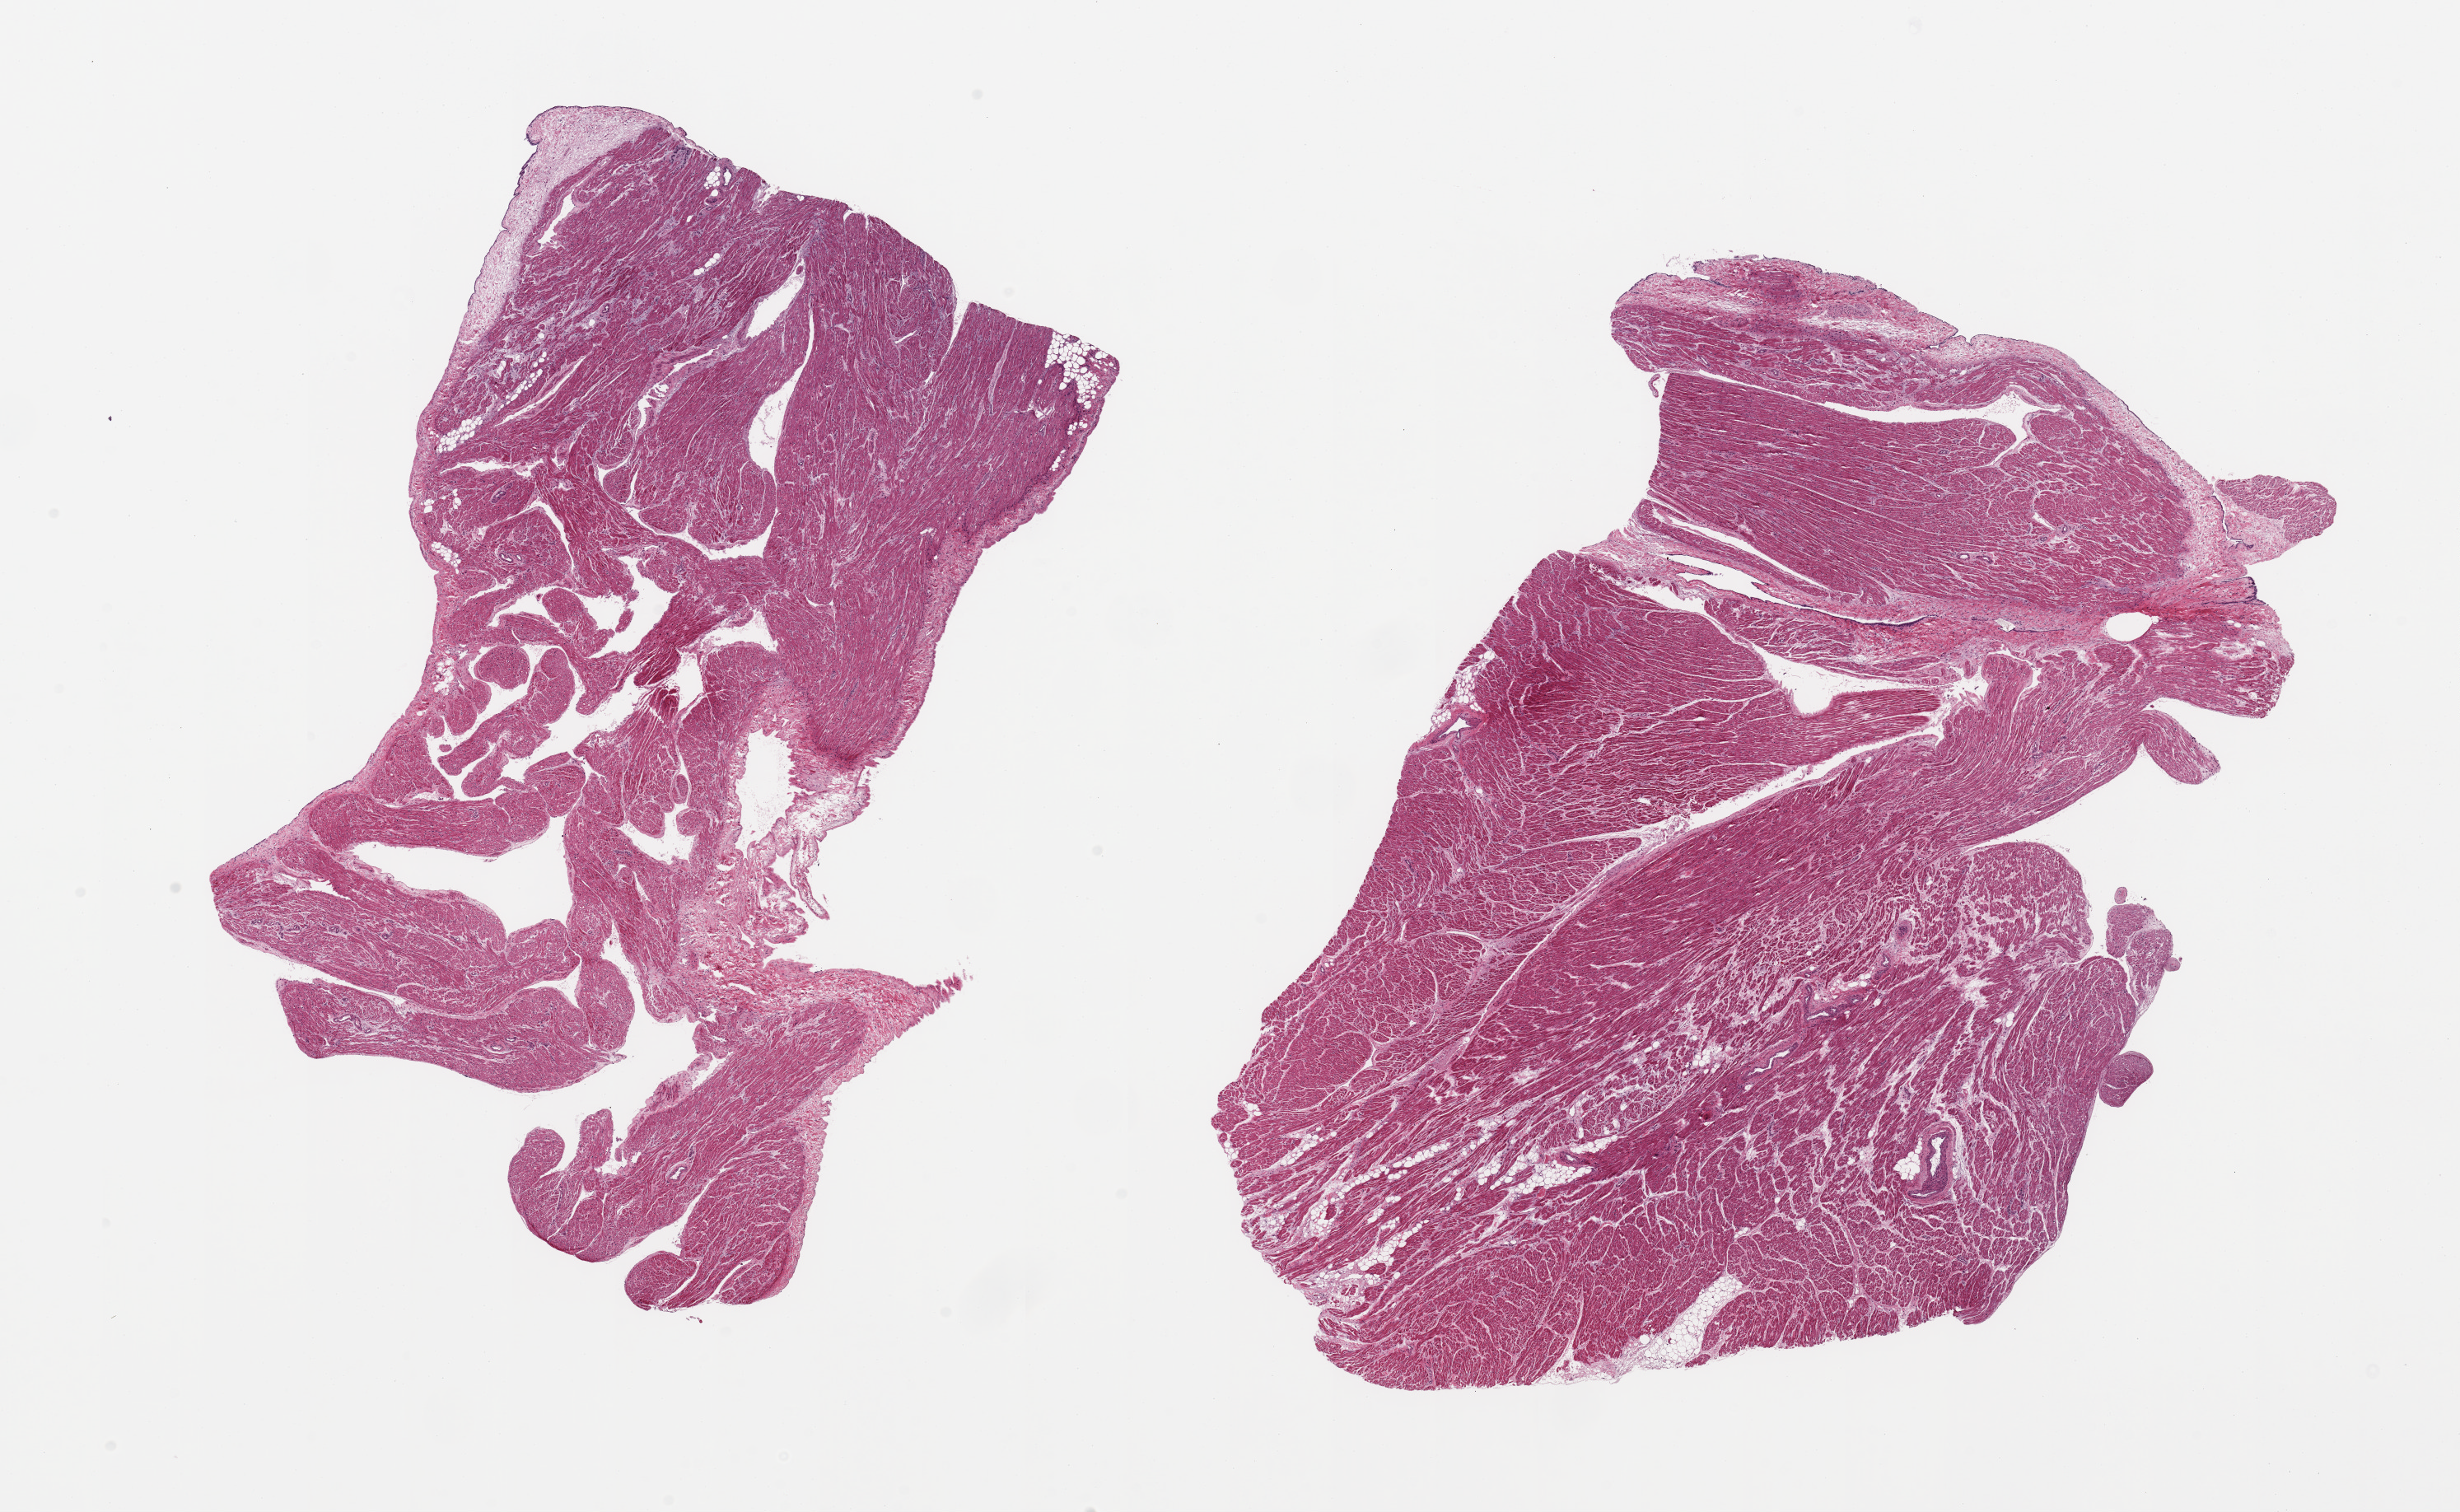
Hematoxylin and eosin (H&E) whole-slide image — a low-resolution overview of the entire scanned area, about 23.6 x 14.5 mm (acquisition: 20x scan). PAXgene-fixed paraffin-embedded (PFPE) section. Target tissue: auricular appendage. Tissue donor sample. Donor sex: male.
Review note (as recorded): 2 pieces, no abnormalities.